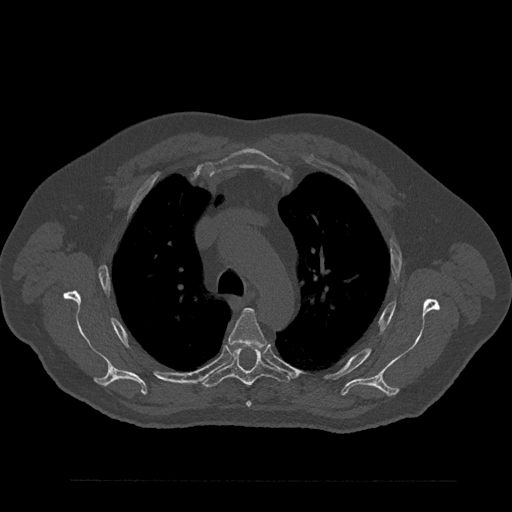
CT including the spine, one axial slice. Position 619 of 797 along the scan axis. Bone window (W 1800 / L 400 HU). 0.5 mm slice thickness. 512 × 512 image matrix, field of view 430 × 430 mm. Patient: male, 61 years. Case-level facts recorded for this patient, not image findings: primary cancer: prostate.
Structures marked on this image (semi-automatically segmented with operator editing):
- T4 vertebra: bounding box [x1, y1, x2, y2] px = [228, 308, 266, 407]
- T5 vertebra: [201, 349, 289, 387]